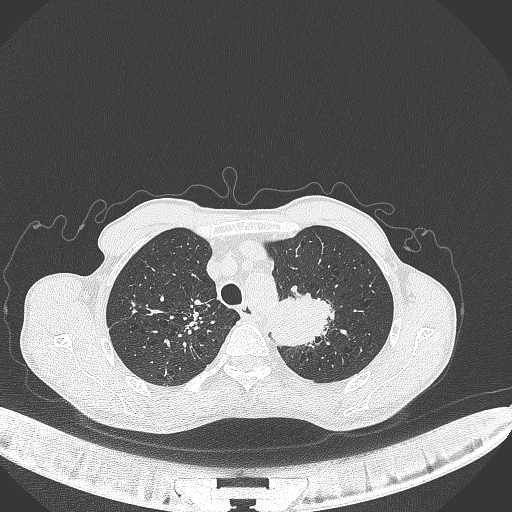
Chest CT, one axial slice. Position 342 of 386 along the scan axis. 120 kVp. Lung window (W 1500 / L -600 HU). 1 mm slice thickness. 512 × 512 image matrix, field of view 400 × 400 mm. Male patient, age 65 years. From the clinical record (not read from this slice): clinical TNM (as recorded): T2b N0 M0; histopathological grade: G2.
Annotated regions visible in this slice (rectangle marked by the reading radiologist):
- lung tumour (recorded histology: adenocarcinoma): bounding box <267,289,335,346> (left, top, right, bottom; pixels)